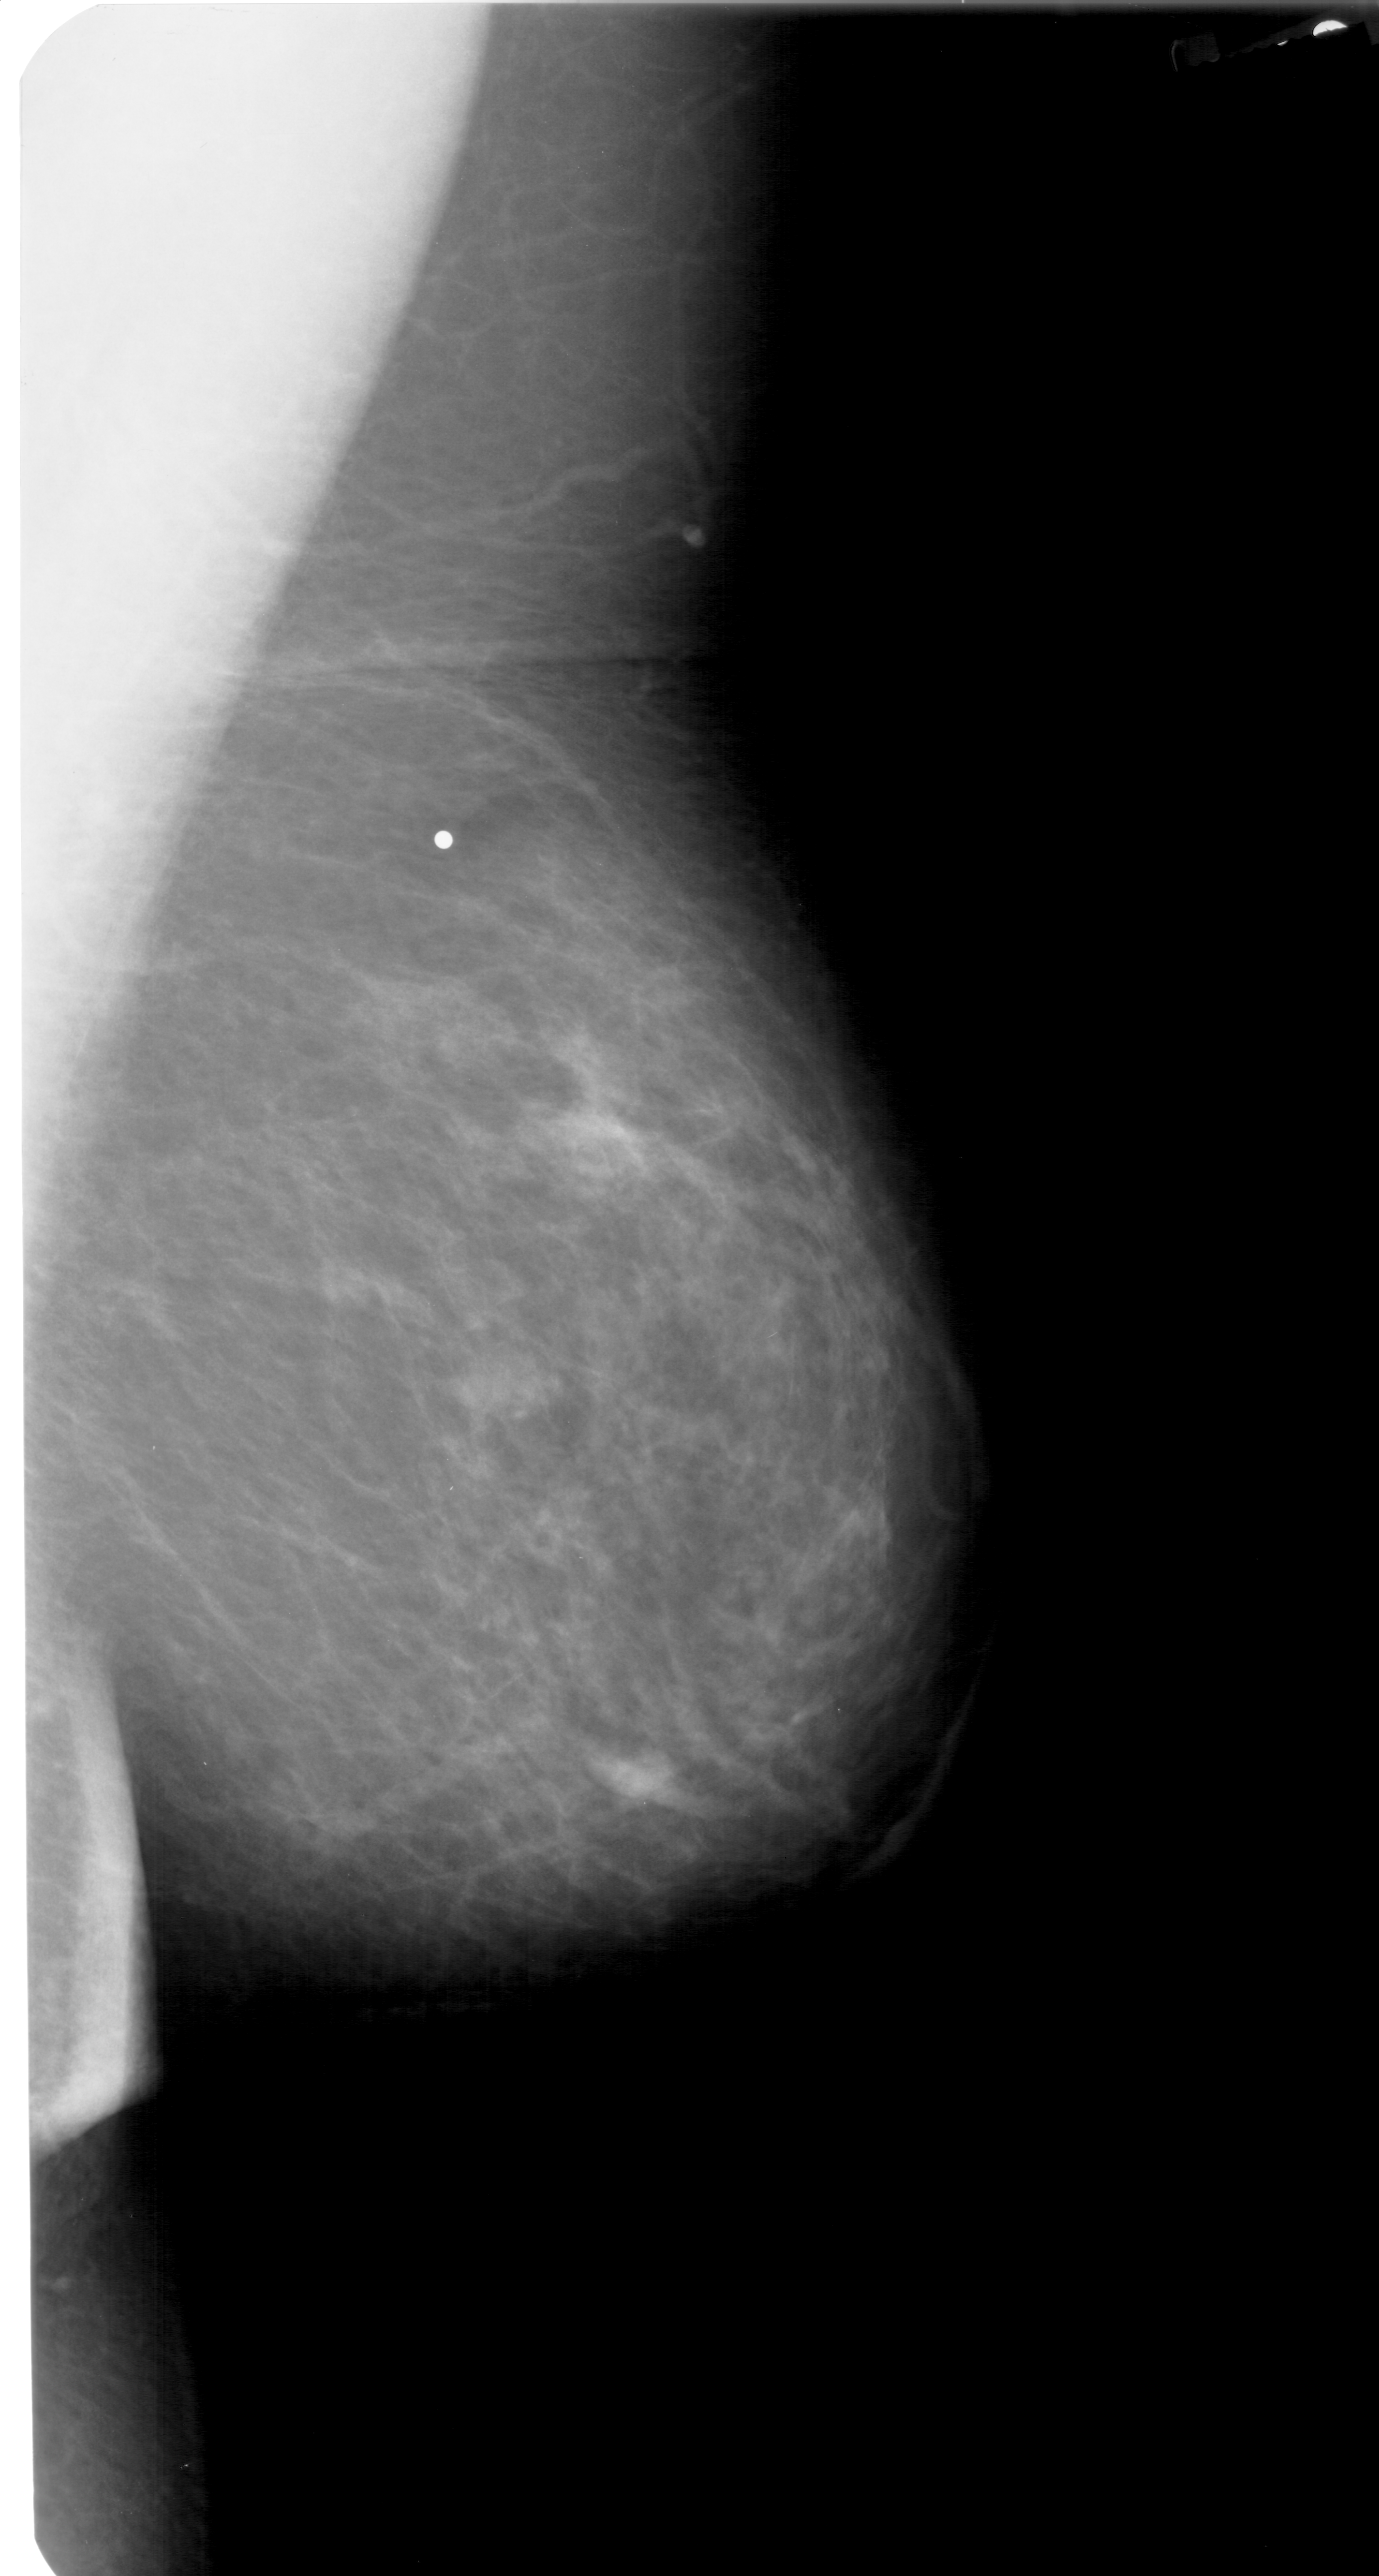
Scanned film-screen mammogram; right breast; MLO view; breast composition: scattered fibroglandular densities (BI-RADS density category 2 of 4).
Finding: mass, shape oval, margins ill defined; BI-RADS assessment category 4; pathology (as recorded): benign.